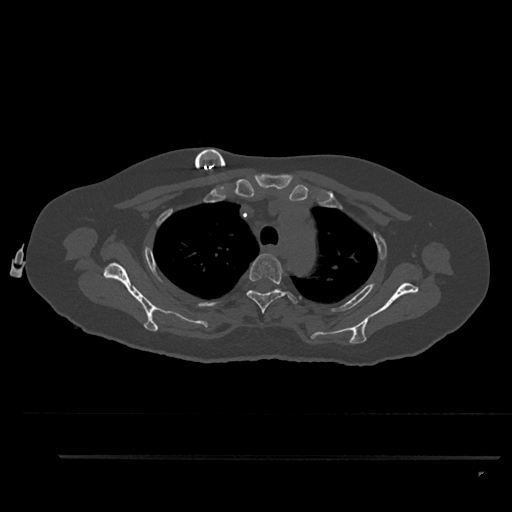
CT including the spine, one axial slice; slice 681 of 797 in the series (ordered by position); reconstruction kernel Br40s/3; 120 kVp; bone window (W 1800 / L 400 HU); 0.5 mm slice thickness; 512 × 512 image matrix, field of view 408 × 408 mm. Patient: female, 44 years. From the clinical record (not read from this slice): primary cancer: renal; vertebrae with lytic lesions (as recorded): L1.
Annotated regions visible in this slice (semi-automatic segmentation, software-assisted and operator-edited):
- T3 vertebra: bounding box [x1, y1, x2, y2] px = [246, 253, 298, 314]